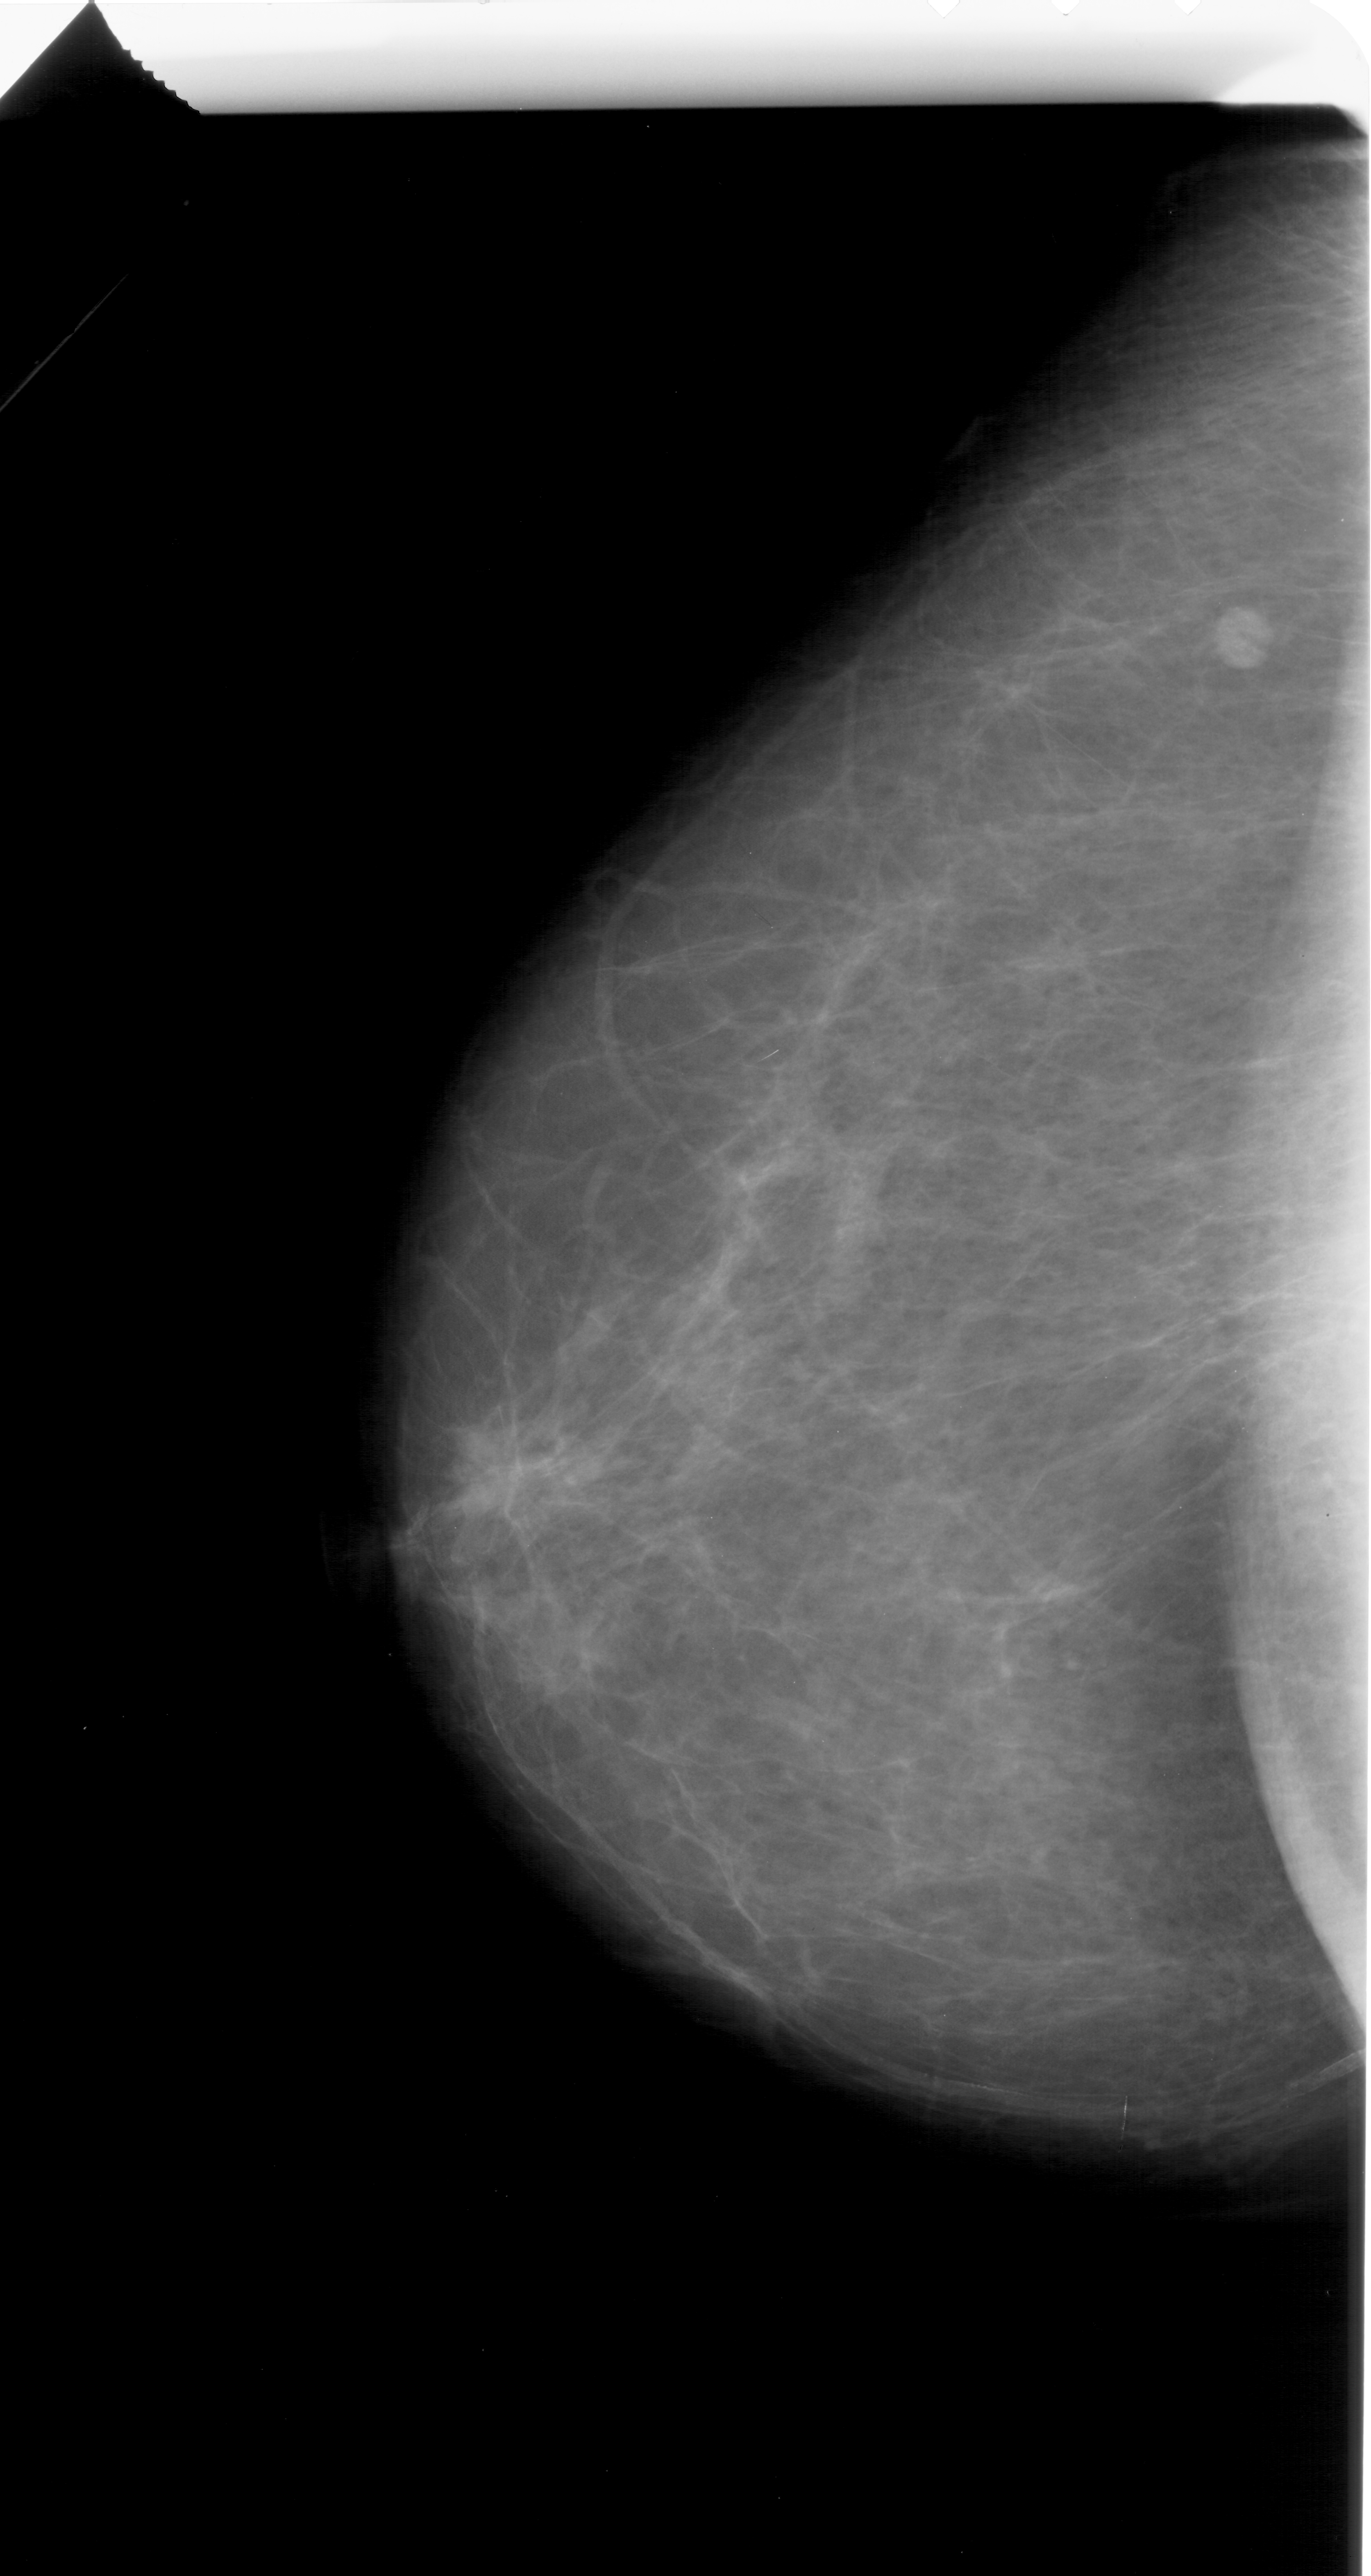
Digitized screen-film mammogram, left breast, craniocaudal (CC) view, BI-RADS breast density category 2 (scale 1–4).
- Abnormality record for this image: mass, shape irregular, margins spiculated; BI-RADS assessment category 5; pathology result (as recorded, not read from the image): malignant.